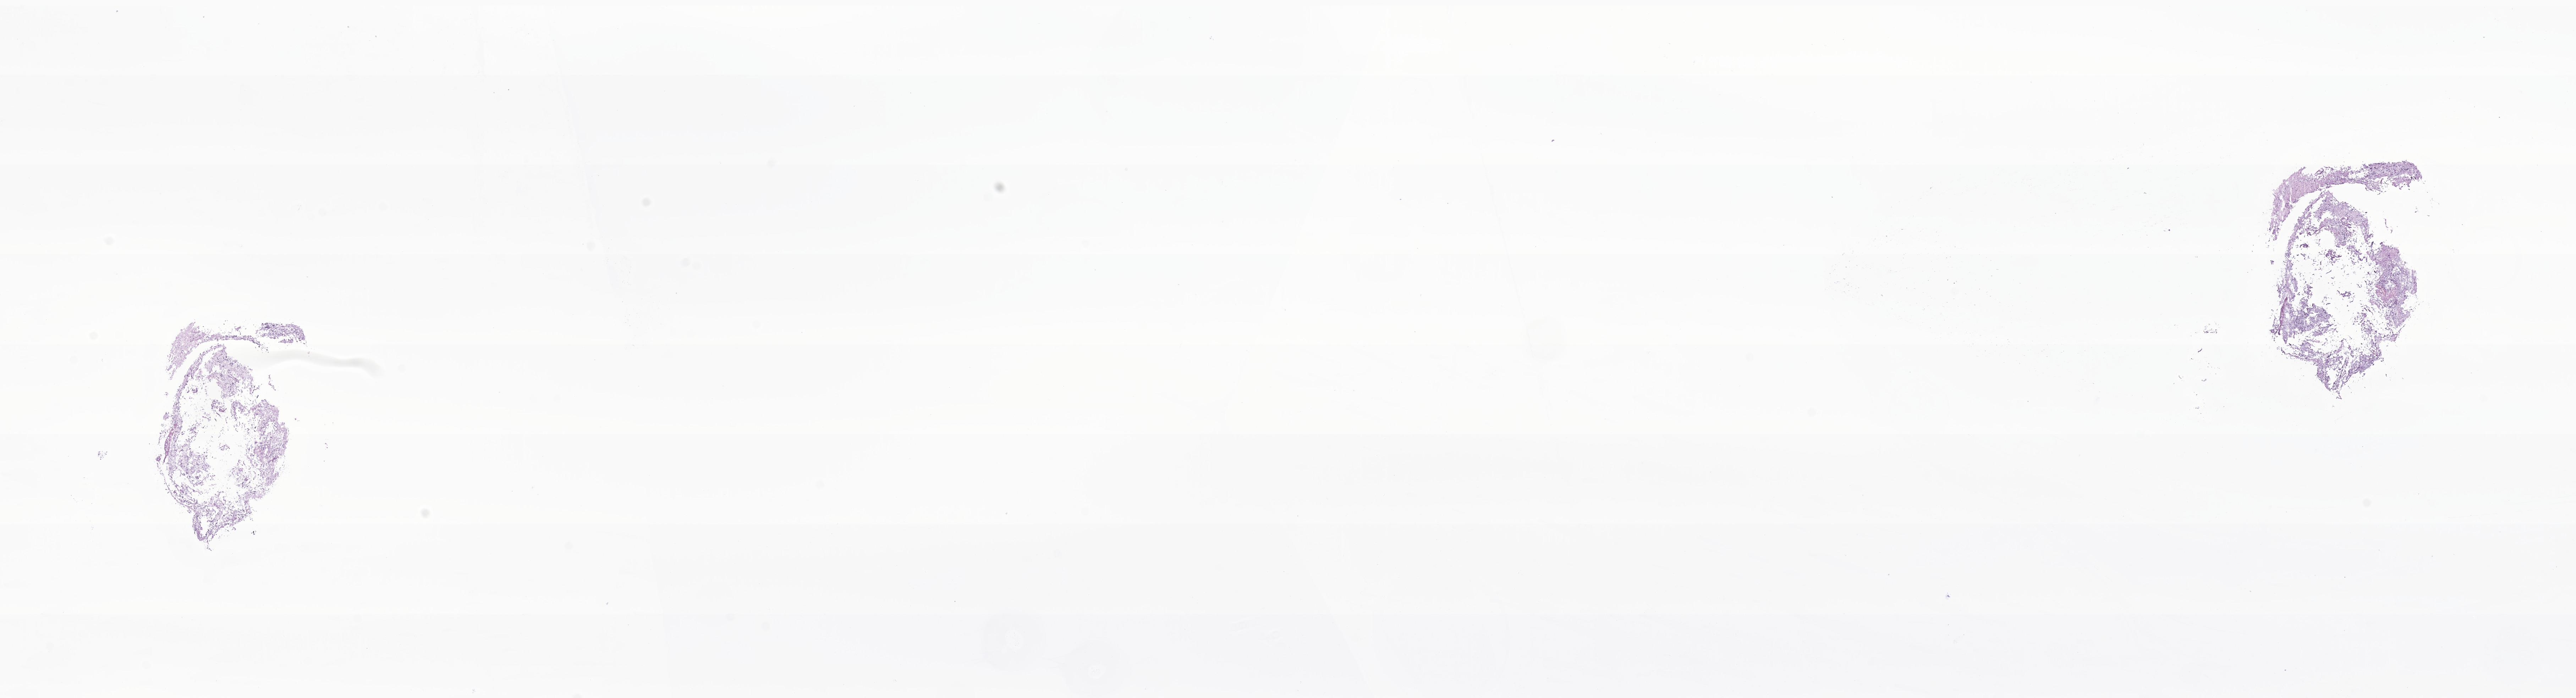
Whole-slide image, hematoxylin and eosin (H&E) stain of tumor tissue from the brain — whole scanned area (about 30.6 x 8.3 mm) shown as a low-resolution overview, cryosection (OCT / tissue freezing medium). Patient: male, age 46 months (3 years 10 months).
• diagnosis (ICD-O-3 morphology term): Tumor cells, uncertain whether benign or malignant